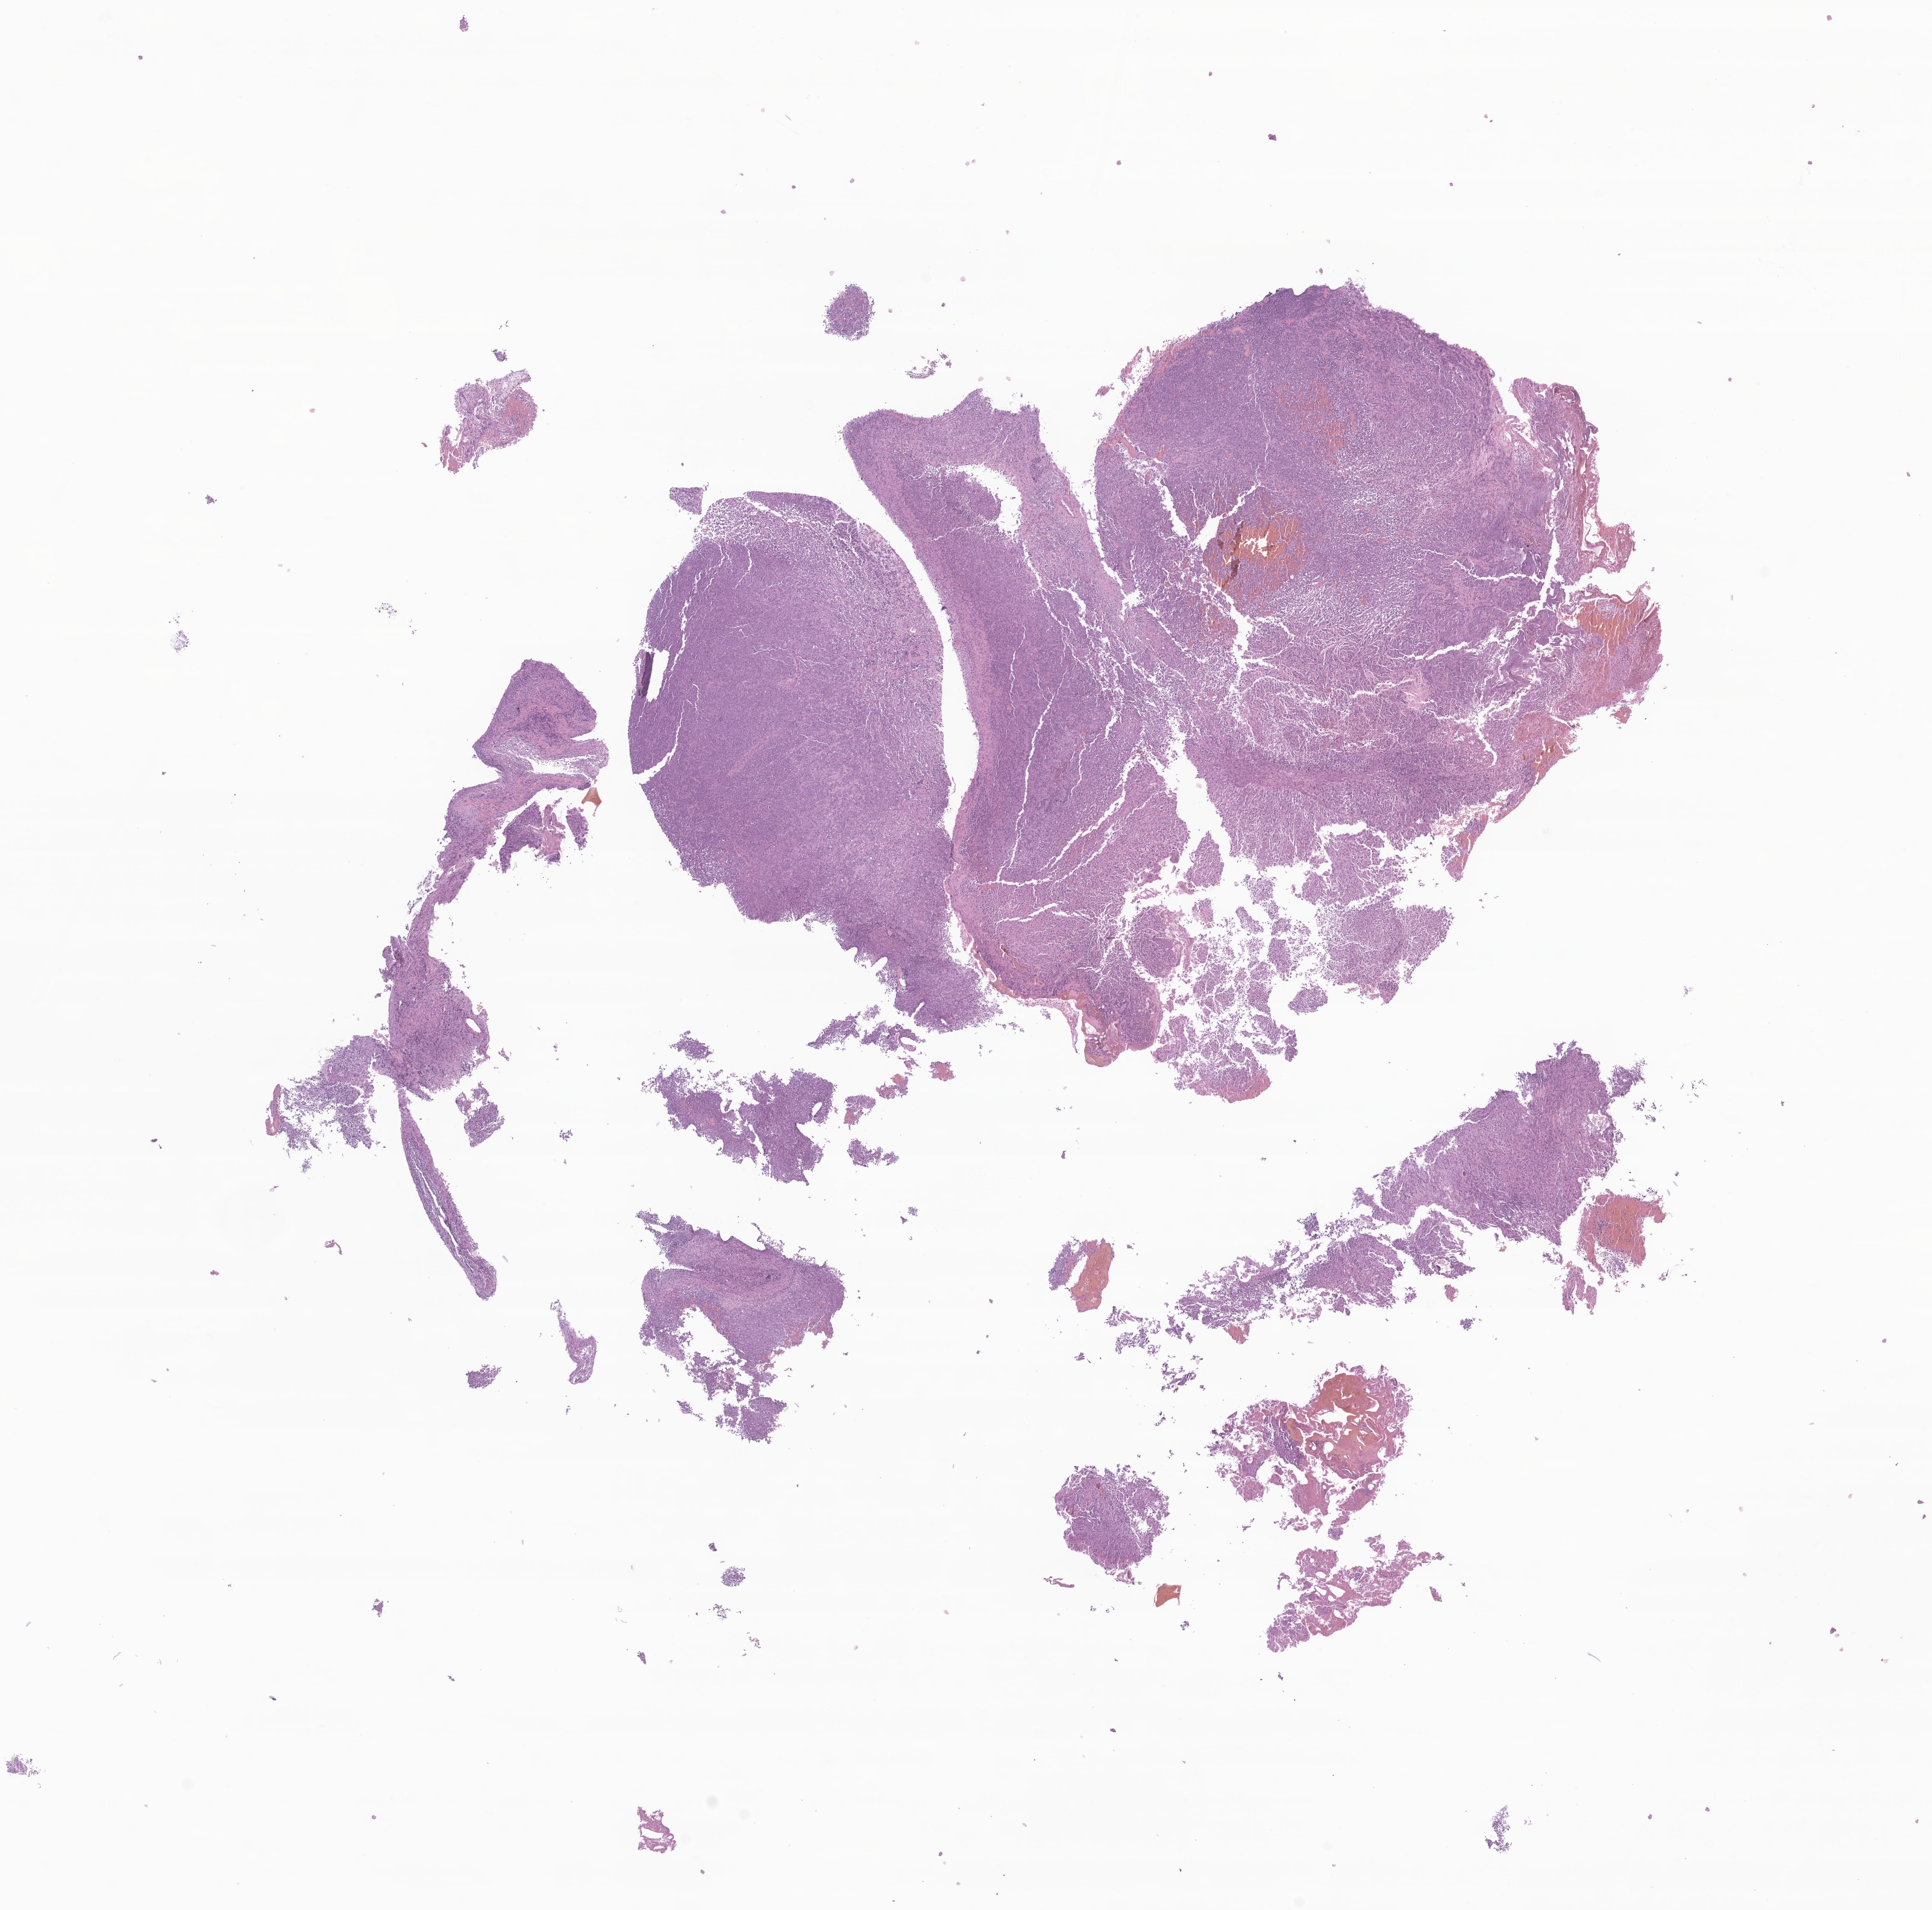
Digitized hematoxylin and eosin (H&E)-stained section of tumor tissue from the cerebellum — shown as a low-resolution overview of the whole scanned area (about 13.5 x 13.4 mm). Formalin-fixed, paraffin-embedded (FFPE) tissue. Patient: female, age 829 days (about 2.3 years).
Diagnosis: Atypical teratoid/rhabdoid tumor.